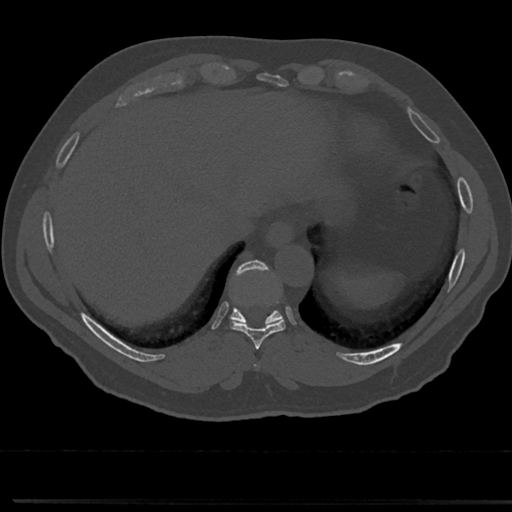
CT including the spine, one axial slice. Slice 289 of 817 in the series (ordered by position). Reconstruction kernel Br40s/3. 120 kVp. Bone window (W 1800 / L 400 HU). 512 × 512 image matrix, field of view 355 × 355 mm. Male patient, age 61 years. From the clinical record (not read from this slice): primary cancer: prostate.
Structures marked on this image (semi-automatic segmentation, software-assisted and operator-edited):
- T8 vertebra: bounding box (x1, y1, x2, y2) in pixels: (255, 342, 264, 371)
- T9 vertebra: (212, 265, 302, 350)